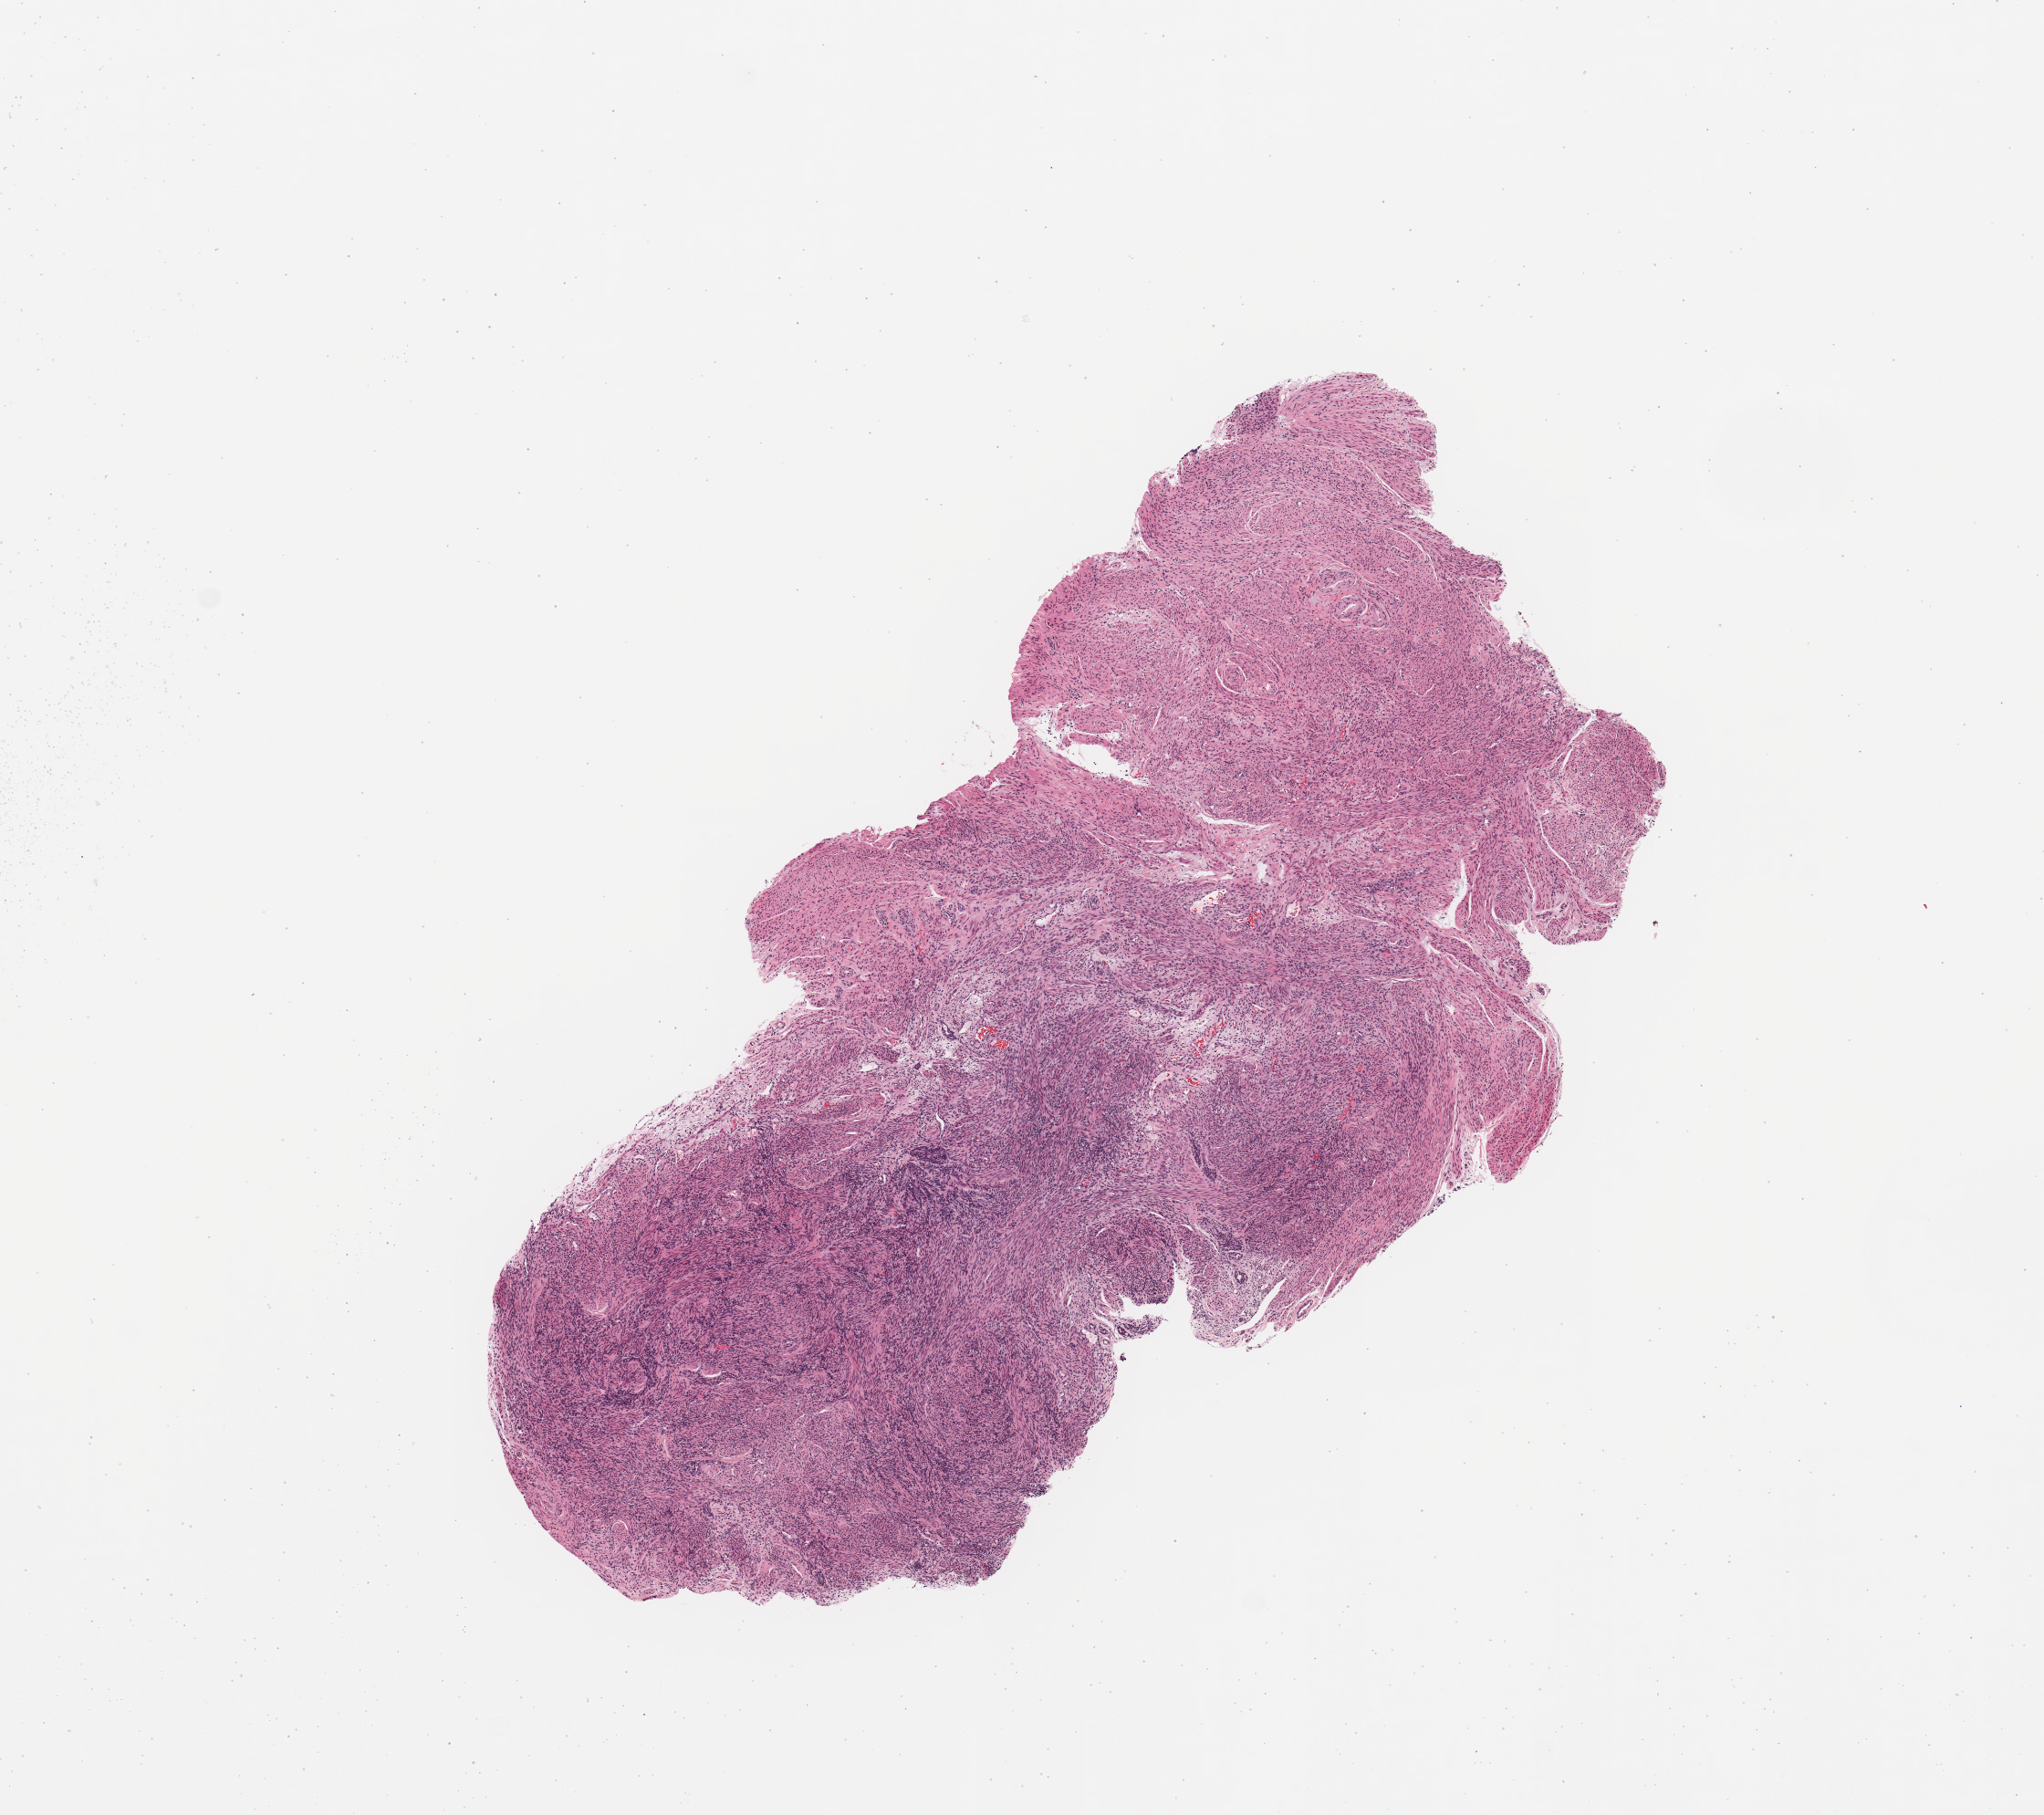
Hematoxylin and eosin (H&E) stained whole-slide image, a low-resolution overview of the entire scanned area, about 8.9 x 7.9 mm (slide scanned at 20x). Normal (non-tumour) tissue sample, sampled site: uterus. Patient: female, age 80 years.
• this section: normal (non-tumour) tissue from the same patient
• patient diagnosis: Endometrioid adenocarcinoma, NOS